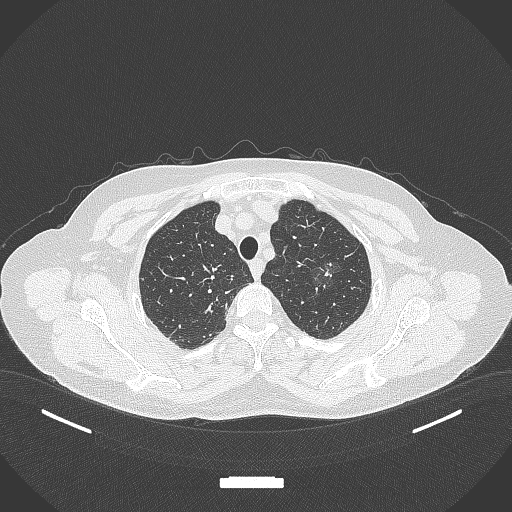
Chest CT, one axial slice; reconstruction kernel B70f; lung window (W 1500 / L -600 HU); 1 mm slice thickness; 512 × 512 image matrix. Female patient, age 64 years. Case-level facts recorded for this patient, not image findings: clinical TNM (as recorded): T1c N0 M0; histopathological grade: G1.
Structures marked on this image (rectangle marked by the reading radiologist):
- lung tumour (recorded histology: adenocarcinoma): bounding box <305,252,340,296> (left, top, right, bottom; pixels)